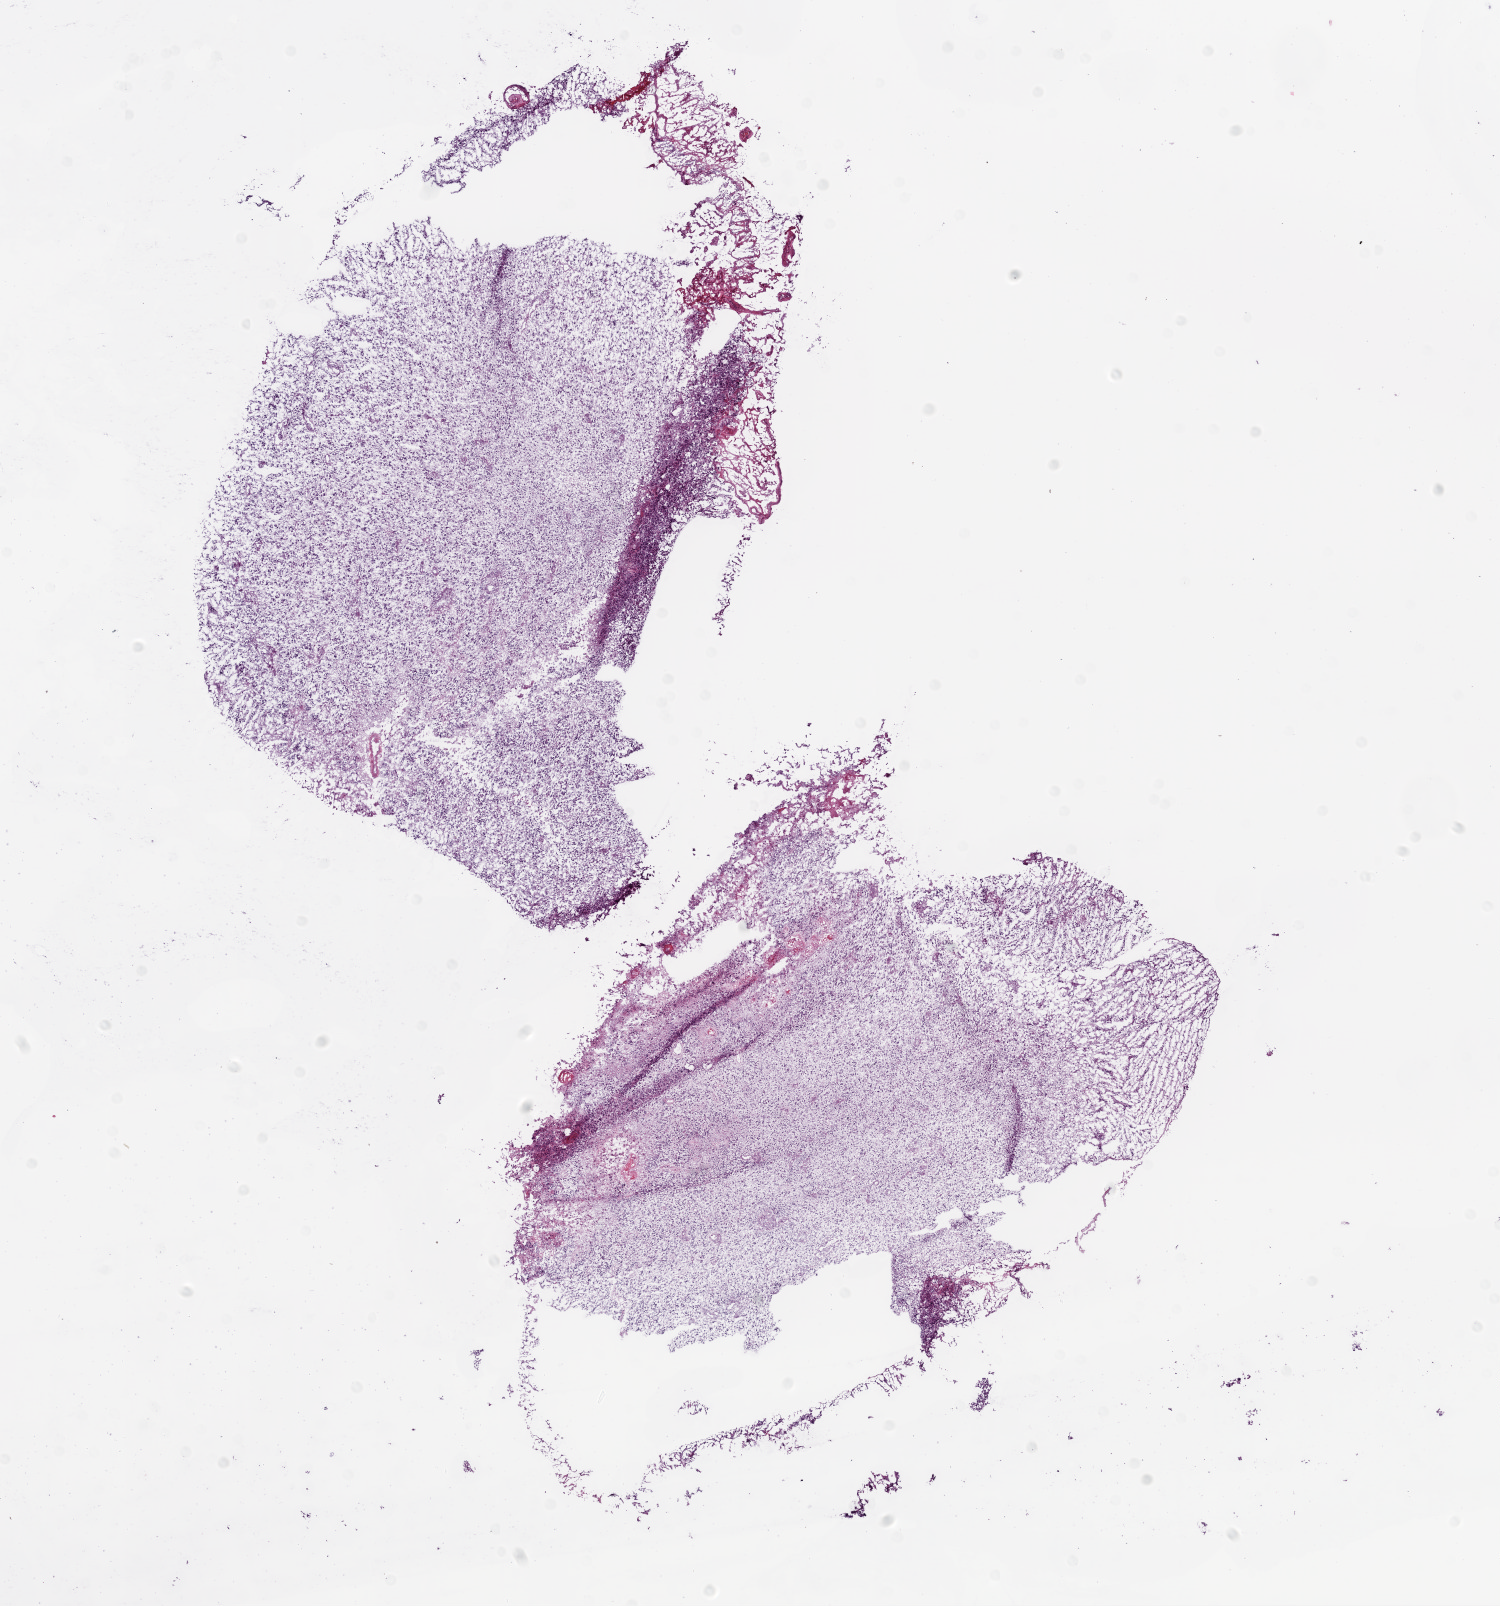
Digitized H&E-stained tissue section (whole slide), shown as a low-resolution overview of the whole scanned area (about 12.0 x 12.9 mm). Frozen section. Primary tumour sample from the brain. Male, age 70 years at initial diagnosis.
Diagnosis: Glioblastoma.